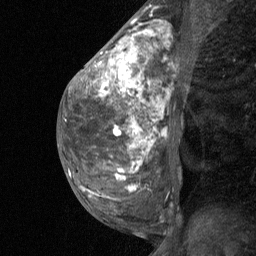
Breast MRI (dynamic contrast-enhanced), one sagittal slice. Position 30 of 64 along the scan axis. Dynamic contrast-enhanced study with each time point stored as its own series, time point 2 of 3 at this slice position (early post-contrast, ordered by acquisition time). 1.5 T. TE 4.8 ms, TR 27 ms. 256 × 256 image matrix, field of view 180 × 180 mm. Patient: female, 36 years. From the clinical record (not read from this slice): setting: breast cancer imaged before/during neoadjuvant chemotherapy; receptor status: HR-positive, HER2-negative.
Outlined on this slice (semi-automatically segmented with operator editing):
- analysis volume of interest (the breast-tissue region the enhancement analysis was run in; not a lesion): bounding box [x1, y1, x2, y2] px = [67, 12, 183, 238]
- tumour enhancement mask (voxels above the 90 % enhancement threshold inside the analysis volume of interest): [82, 29, 155, 188]